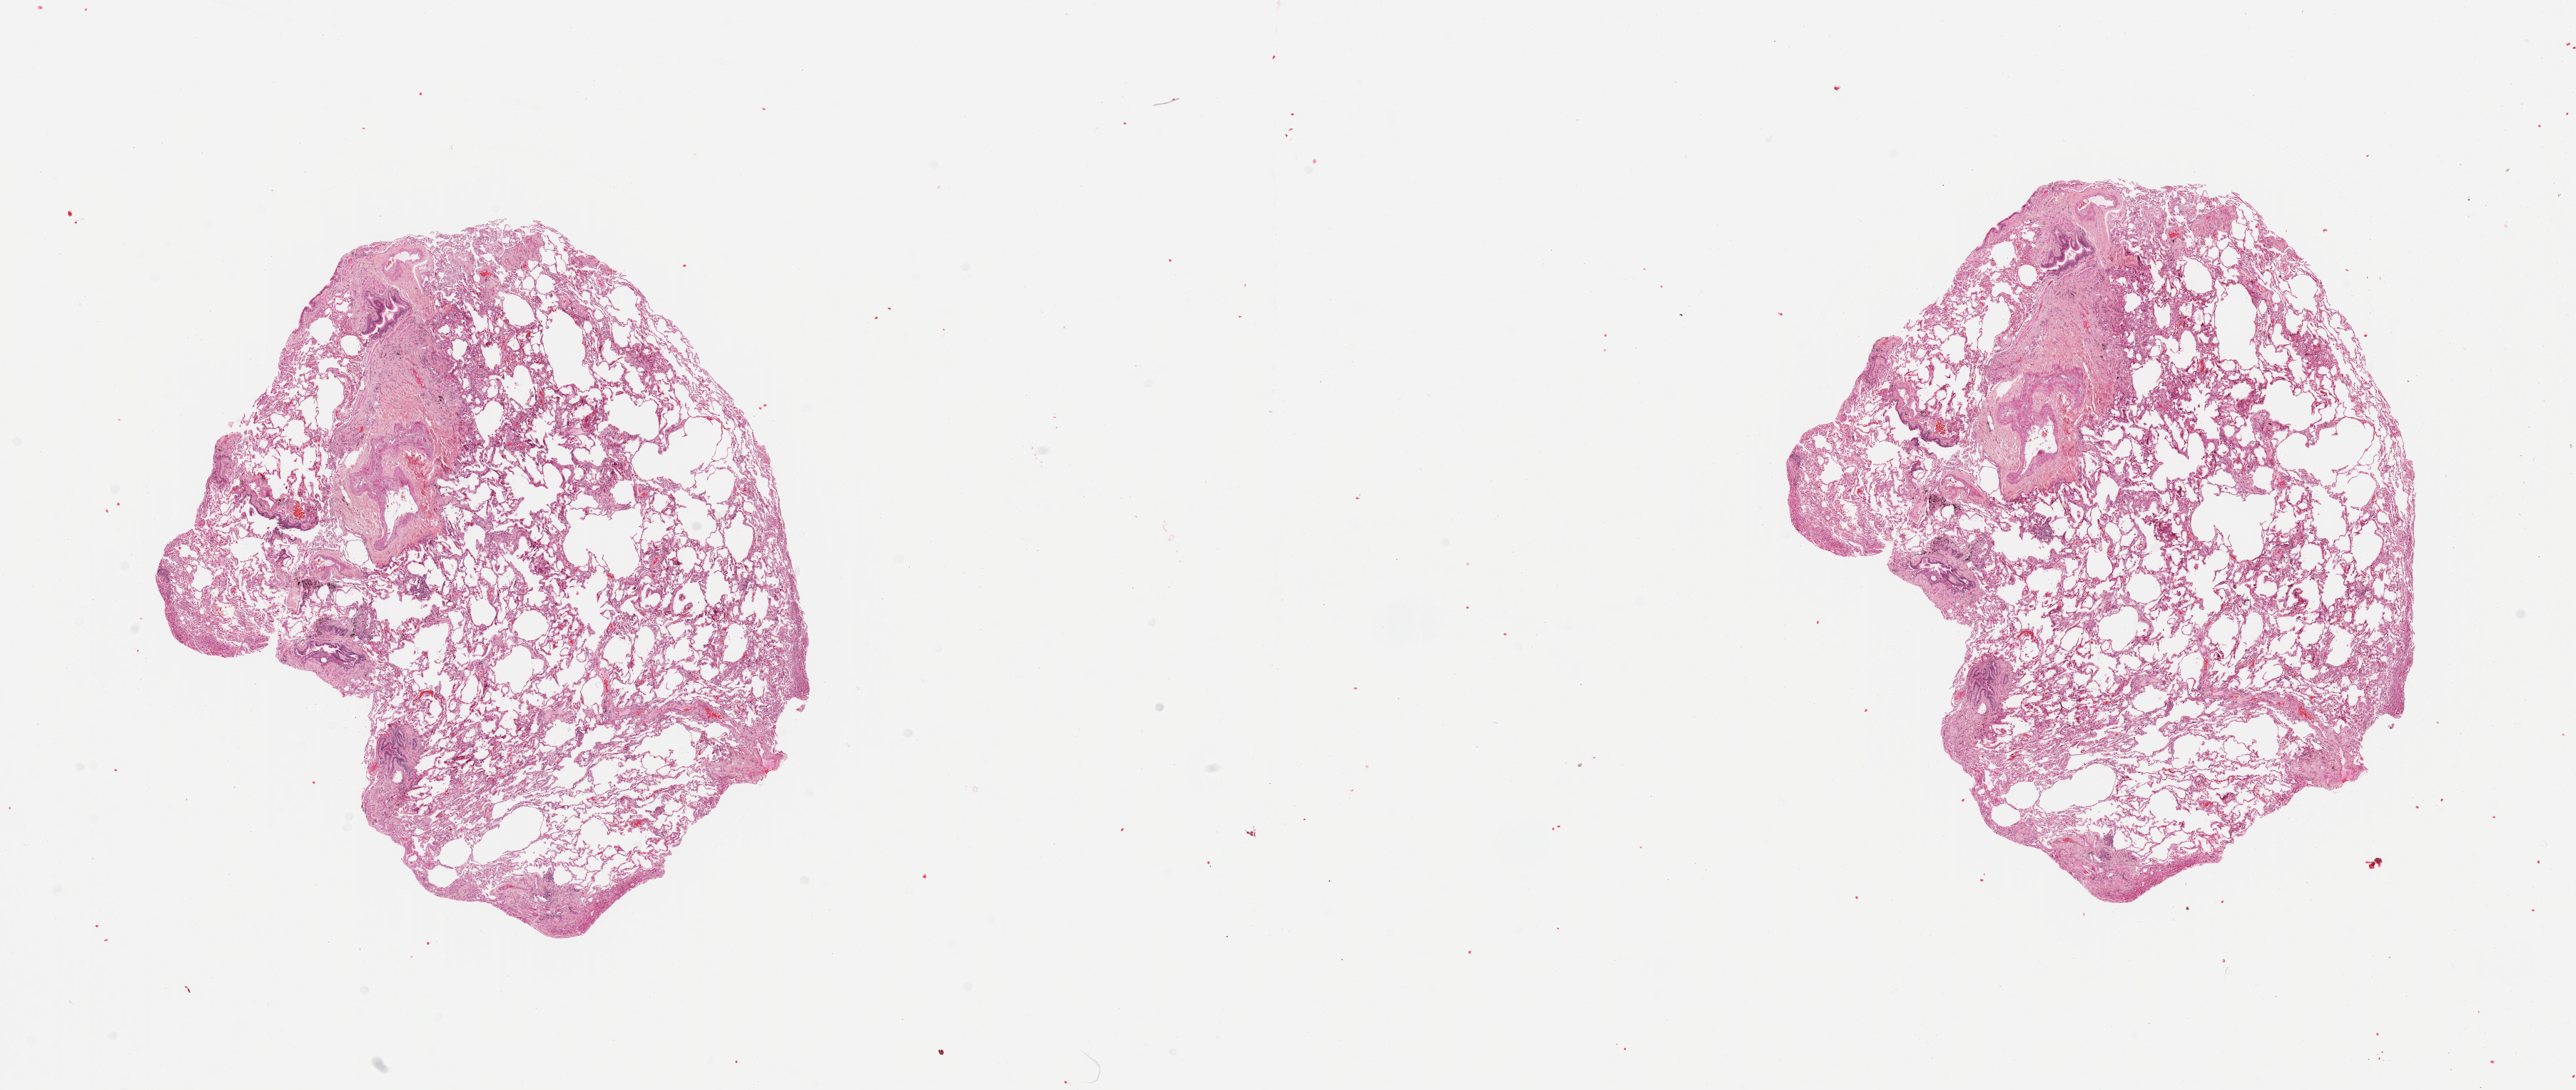
H&E whole-slide image, whole scanned area (about 28.5 x 12.1 mm, slide scanned at 20x) shown as a low-resolution overview, lung, normal (non-tumour) tissue. 69-year-old female patient.
• this section: normal (non-tumour) tissue from the same patient
• patient diagnosis: Adenocarcinoma, NOS